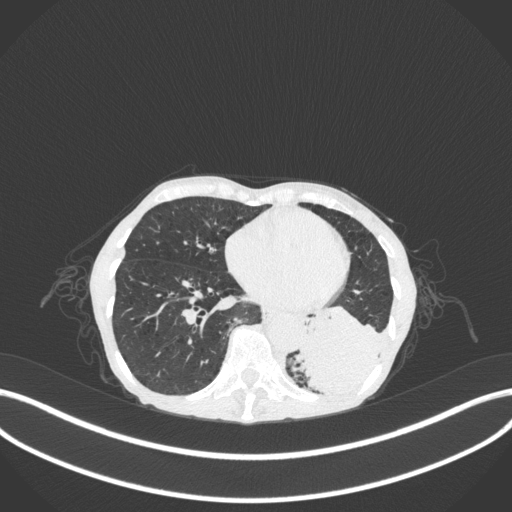
Chest CT, one axial slice. Slice 89 of 347 in the series (ordered by position). Reconstruction kernel B31f. Lung window (W 1500 / L -600 HU). 512 × 512 image matrix, field of view 400 × 400 mm. Patient: female, 70 years. Case-level facts recorded for this patient, not image findings: clinical TNM (as recorded): T3 N0 M0; histopathological grade: G3.
Annotated regions visible in this slice (bounding box drawn by a radiologist):
- lung tumour (recorded histology: small cell carcinoma): box from (x=294, y=300) to (x=387, y=396) px